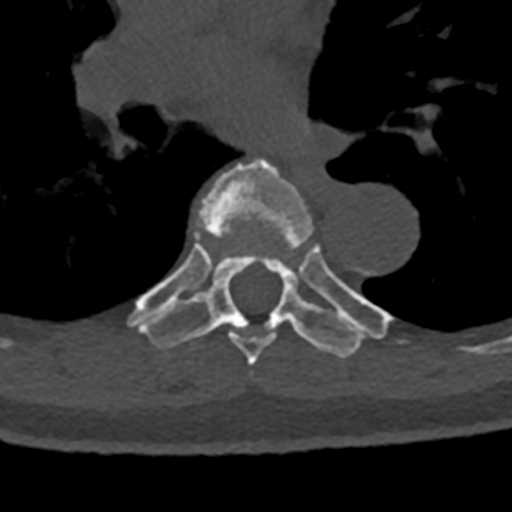
CT including the spine, one axial slice; reconstruction kernel Br40s/3; bone window (W 1800 / L 400 HU); 0.5 mm slice thickness; 512 × 512 image matrix, field of view 160 × 160 mm. Male patient, age 74 years. From the clinical record (not read from this slice): primary cancer: renal; vertebrae with lytic lesions (as recorded): T10, L1, L2, L3, L4, L5.
Structures marked on this image (semi-automatically segmented with operator editing):
- T6 vertebra: bounding box (x1, y1, x2, y2) in pixels: (171, 158, 314, 366)
- T7 vertebra: (128, 236, 391, 359)